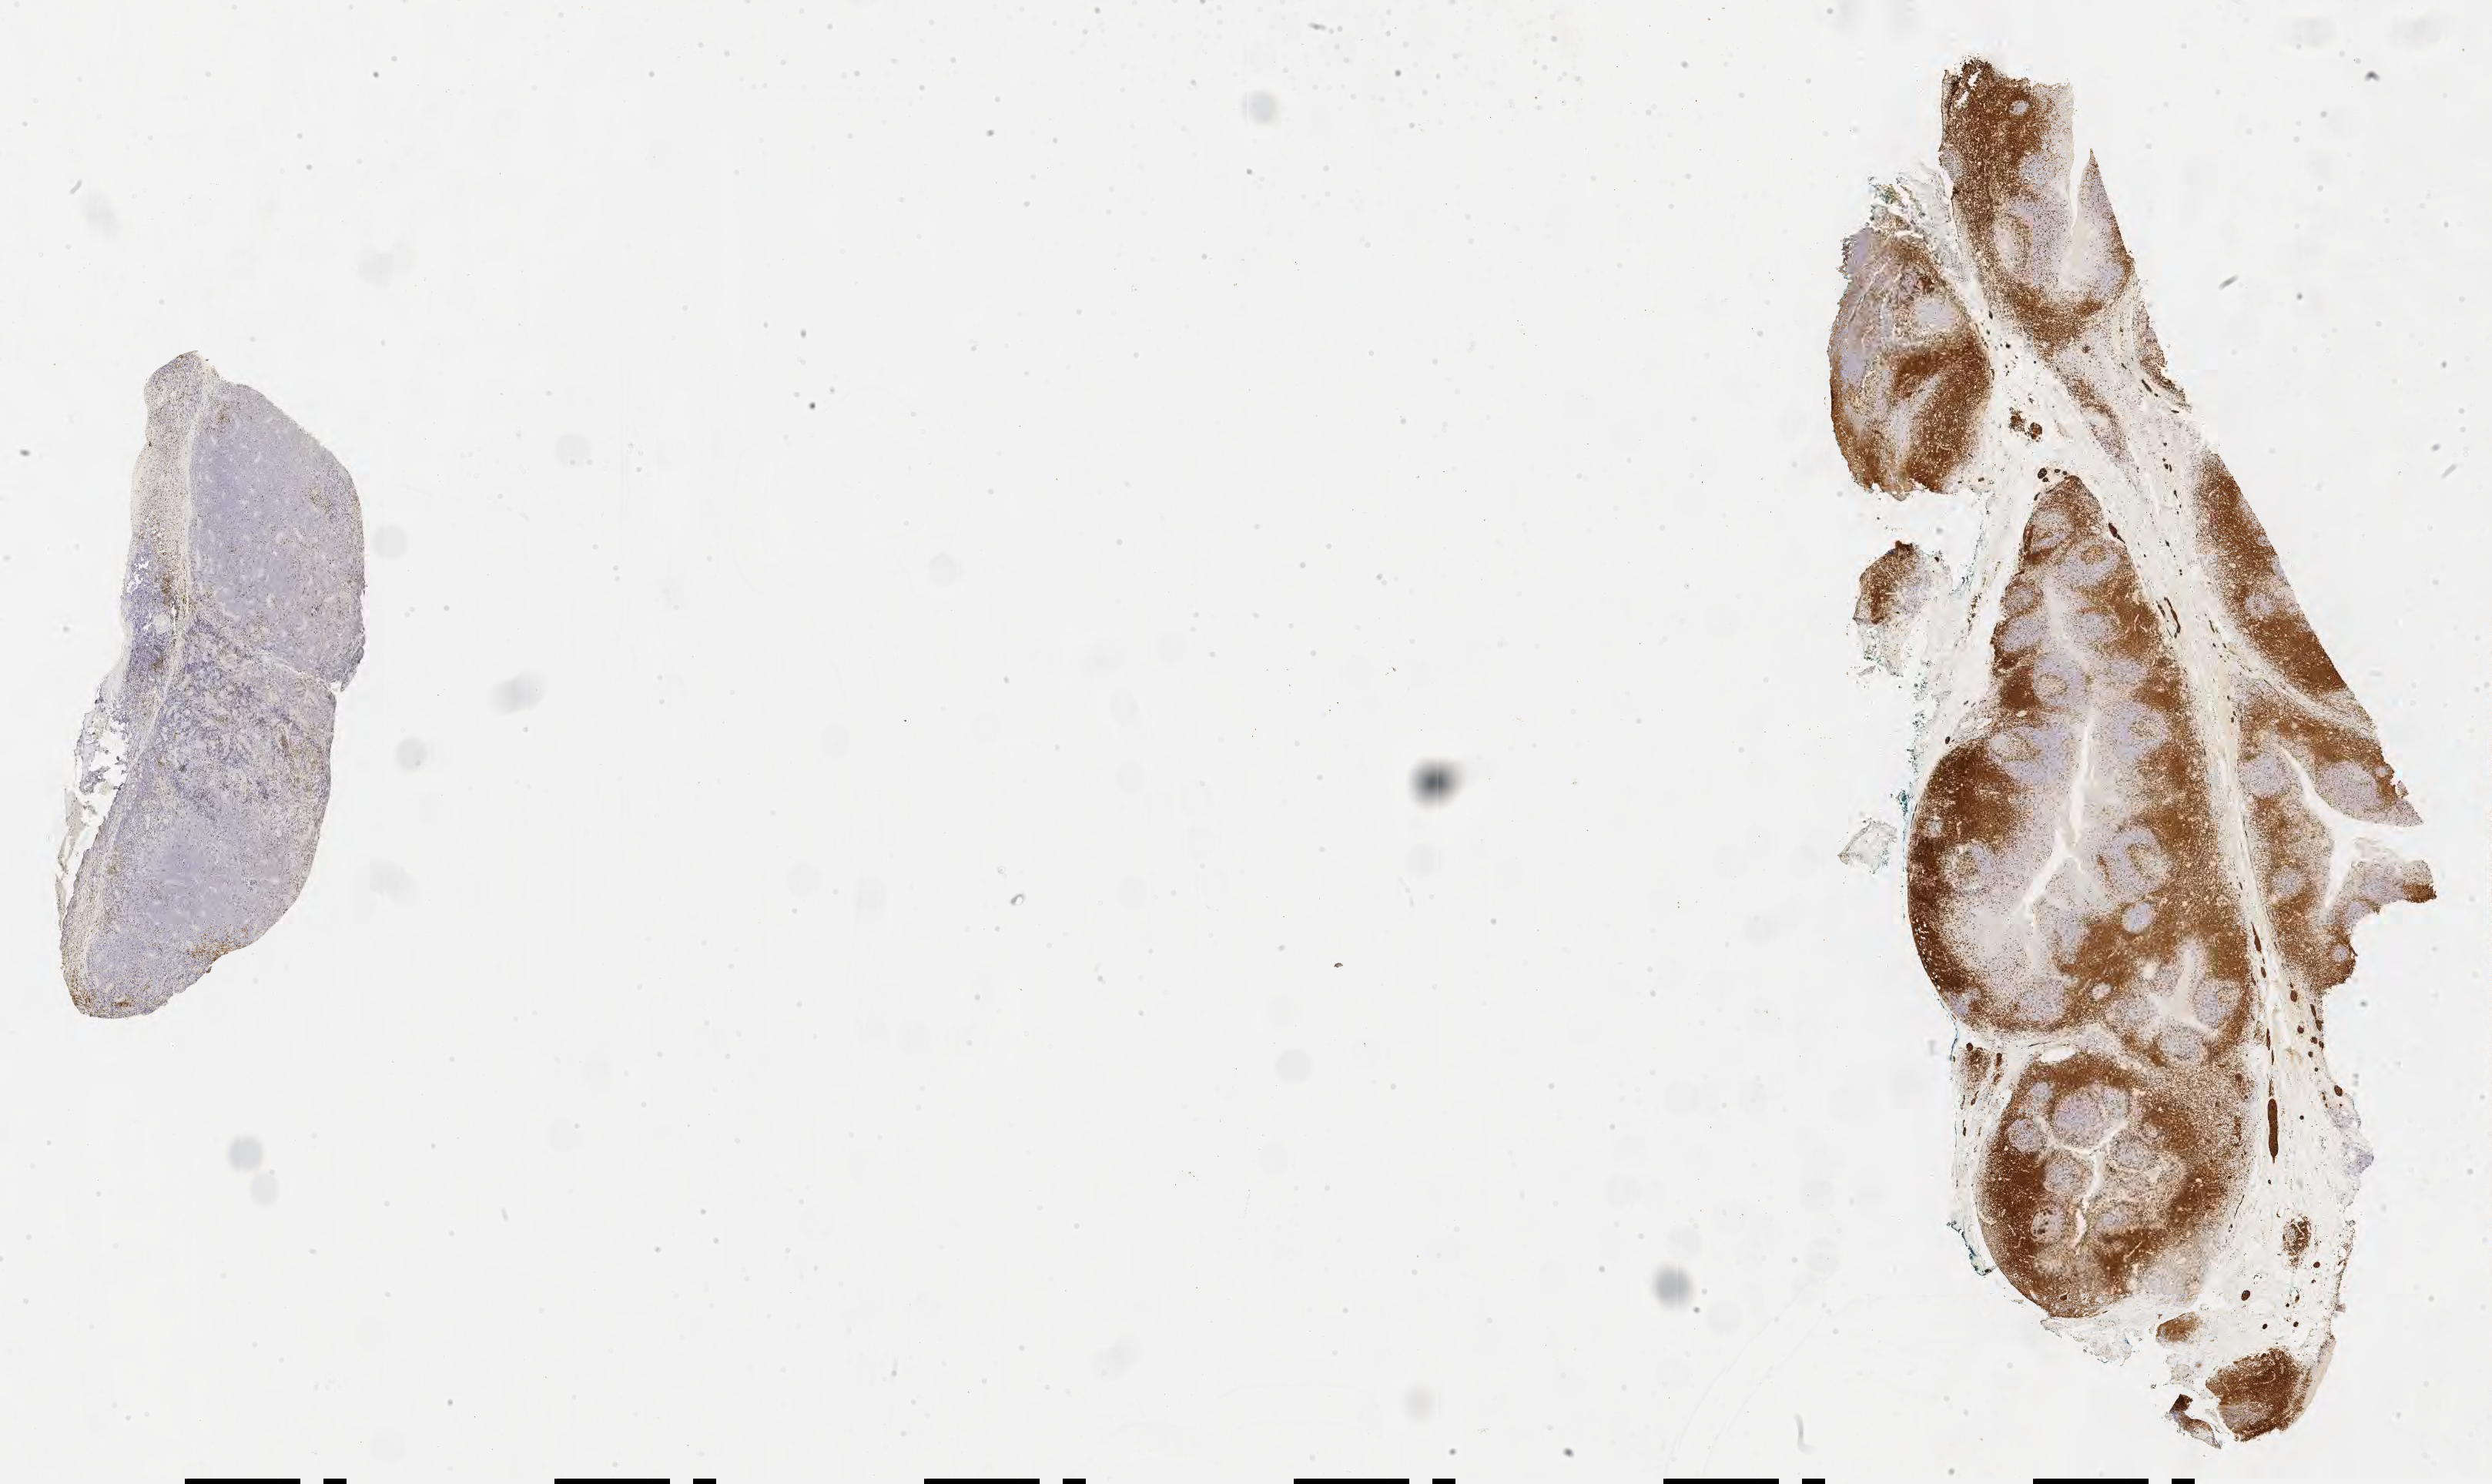
Whole-slide image, immunohistochemical stain for CD3 — whole scanned area (about 26.2 x 15.6 mm) shown as a low-resolution overview, specimen: tumor tissue, site: testis. Male patient; age at initial diagnosis 8 years.
Histologic diagnosis: Burkitt lymphoma, NOS.